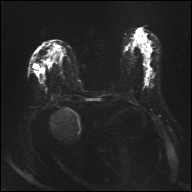
Breast MRI, one axial slice. Diffusion-weighted series; image 2 of 4 stored at this slice position (different b-values; order by instance number). 1.5 T. 4 mm slice thickness. 192 × 192 image matrix, field of view 360 × 360 mm. Female patient.
Structures marked on this image (outlined manually by an expert reader):
- tumour on diffusion-weighted imaging: bounding box [x1, y1, x2, y2] px = [147, 80, 149, 82]